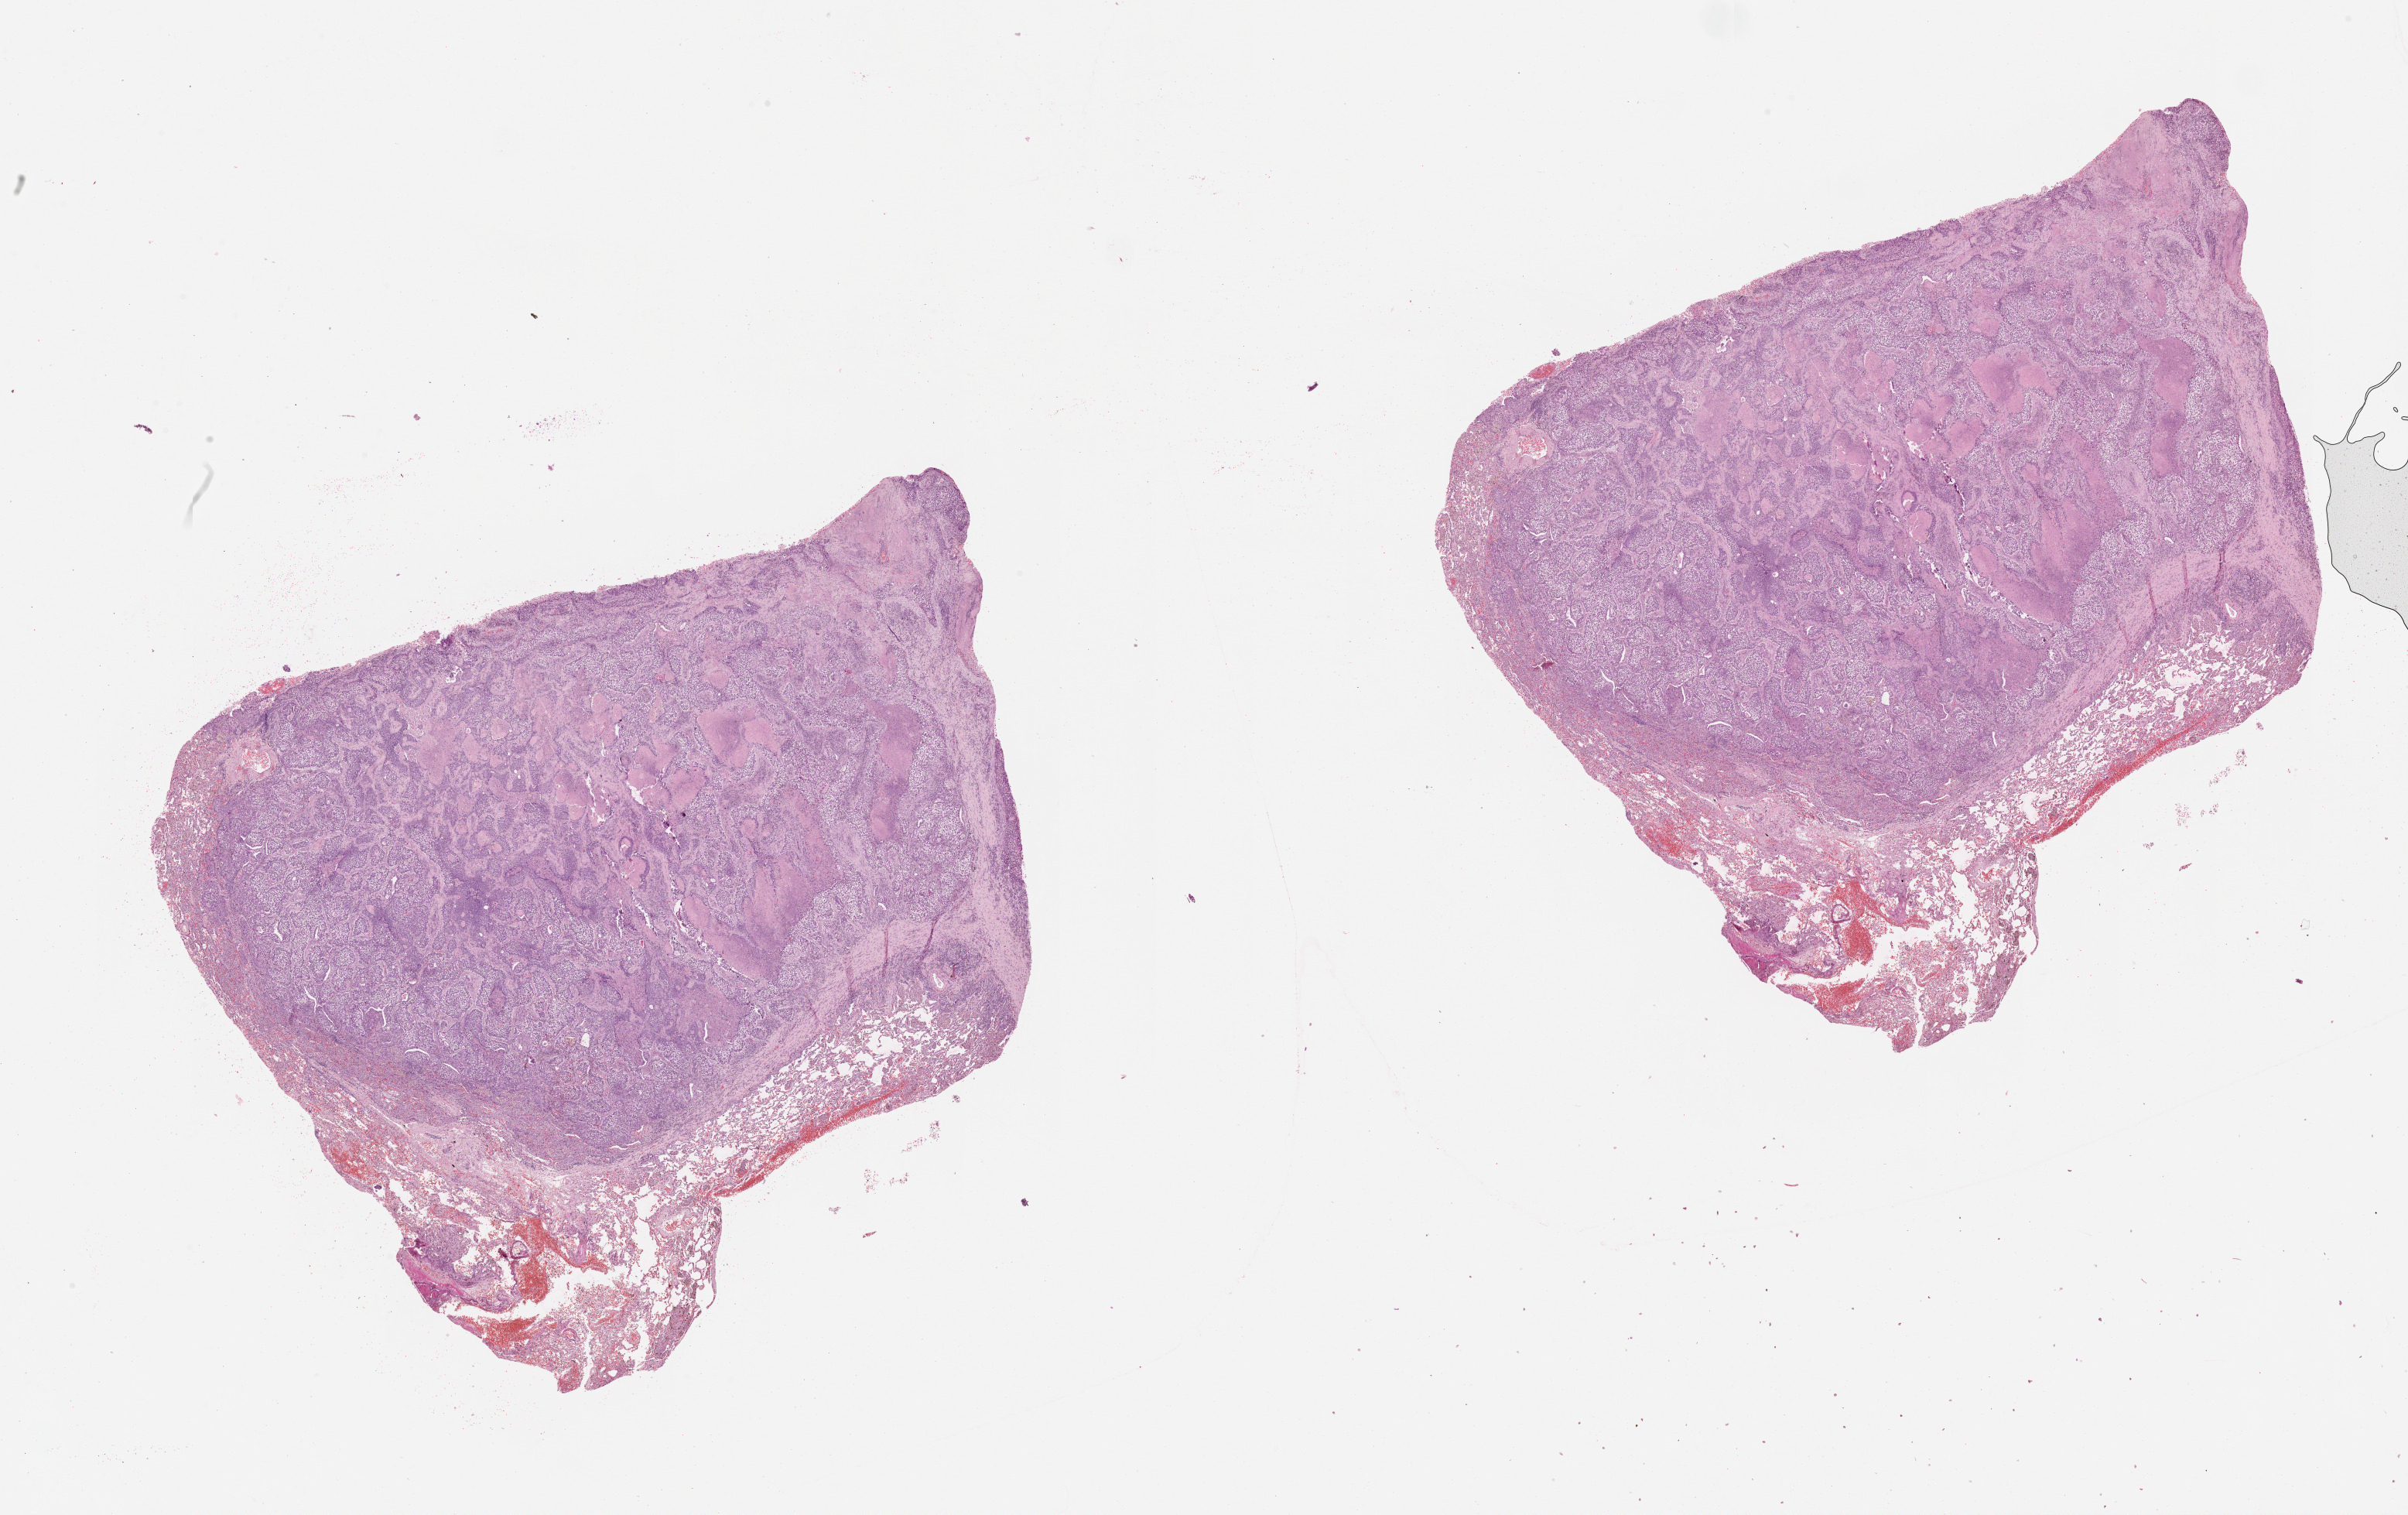
H&E whole-slide image — shown as a low-resolution overview of the whole scanned area (about 25.1 x 15.8 mm); tumour tissue sample, lung. Male, 56 y/o.
Patient diagnosis (cohort enrolment): squamous cell carcinoma (lung).